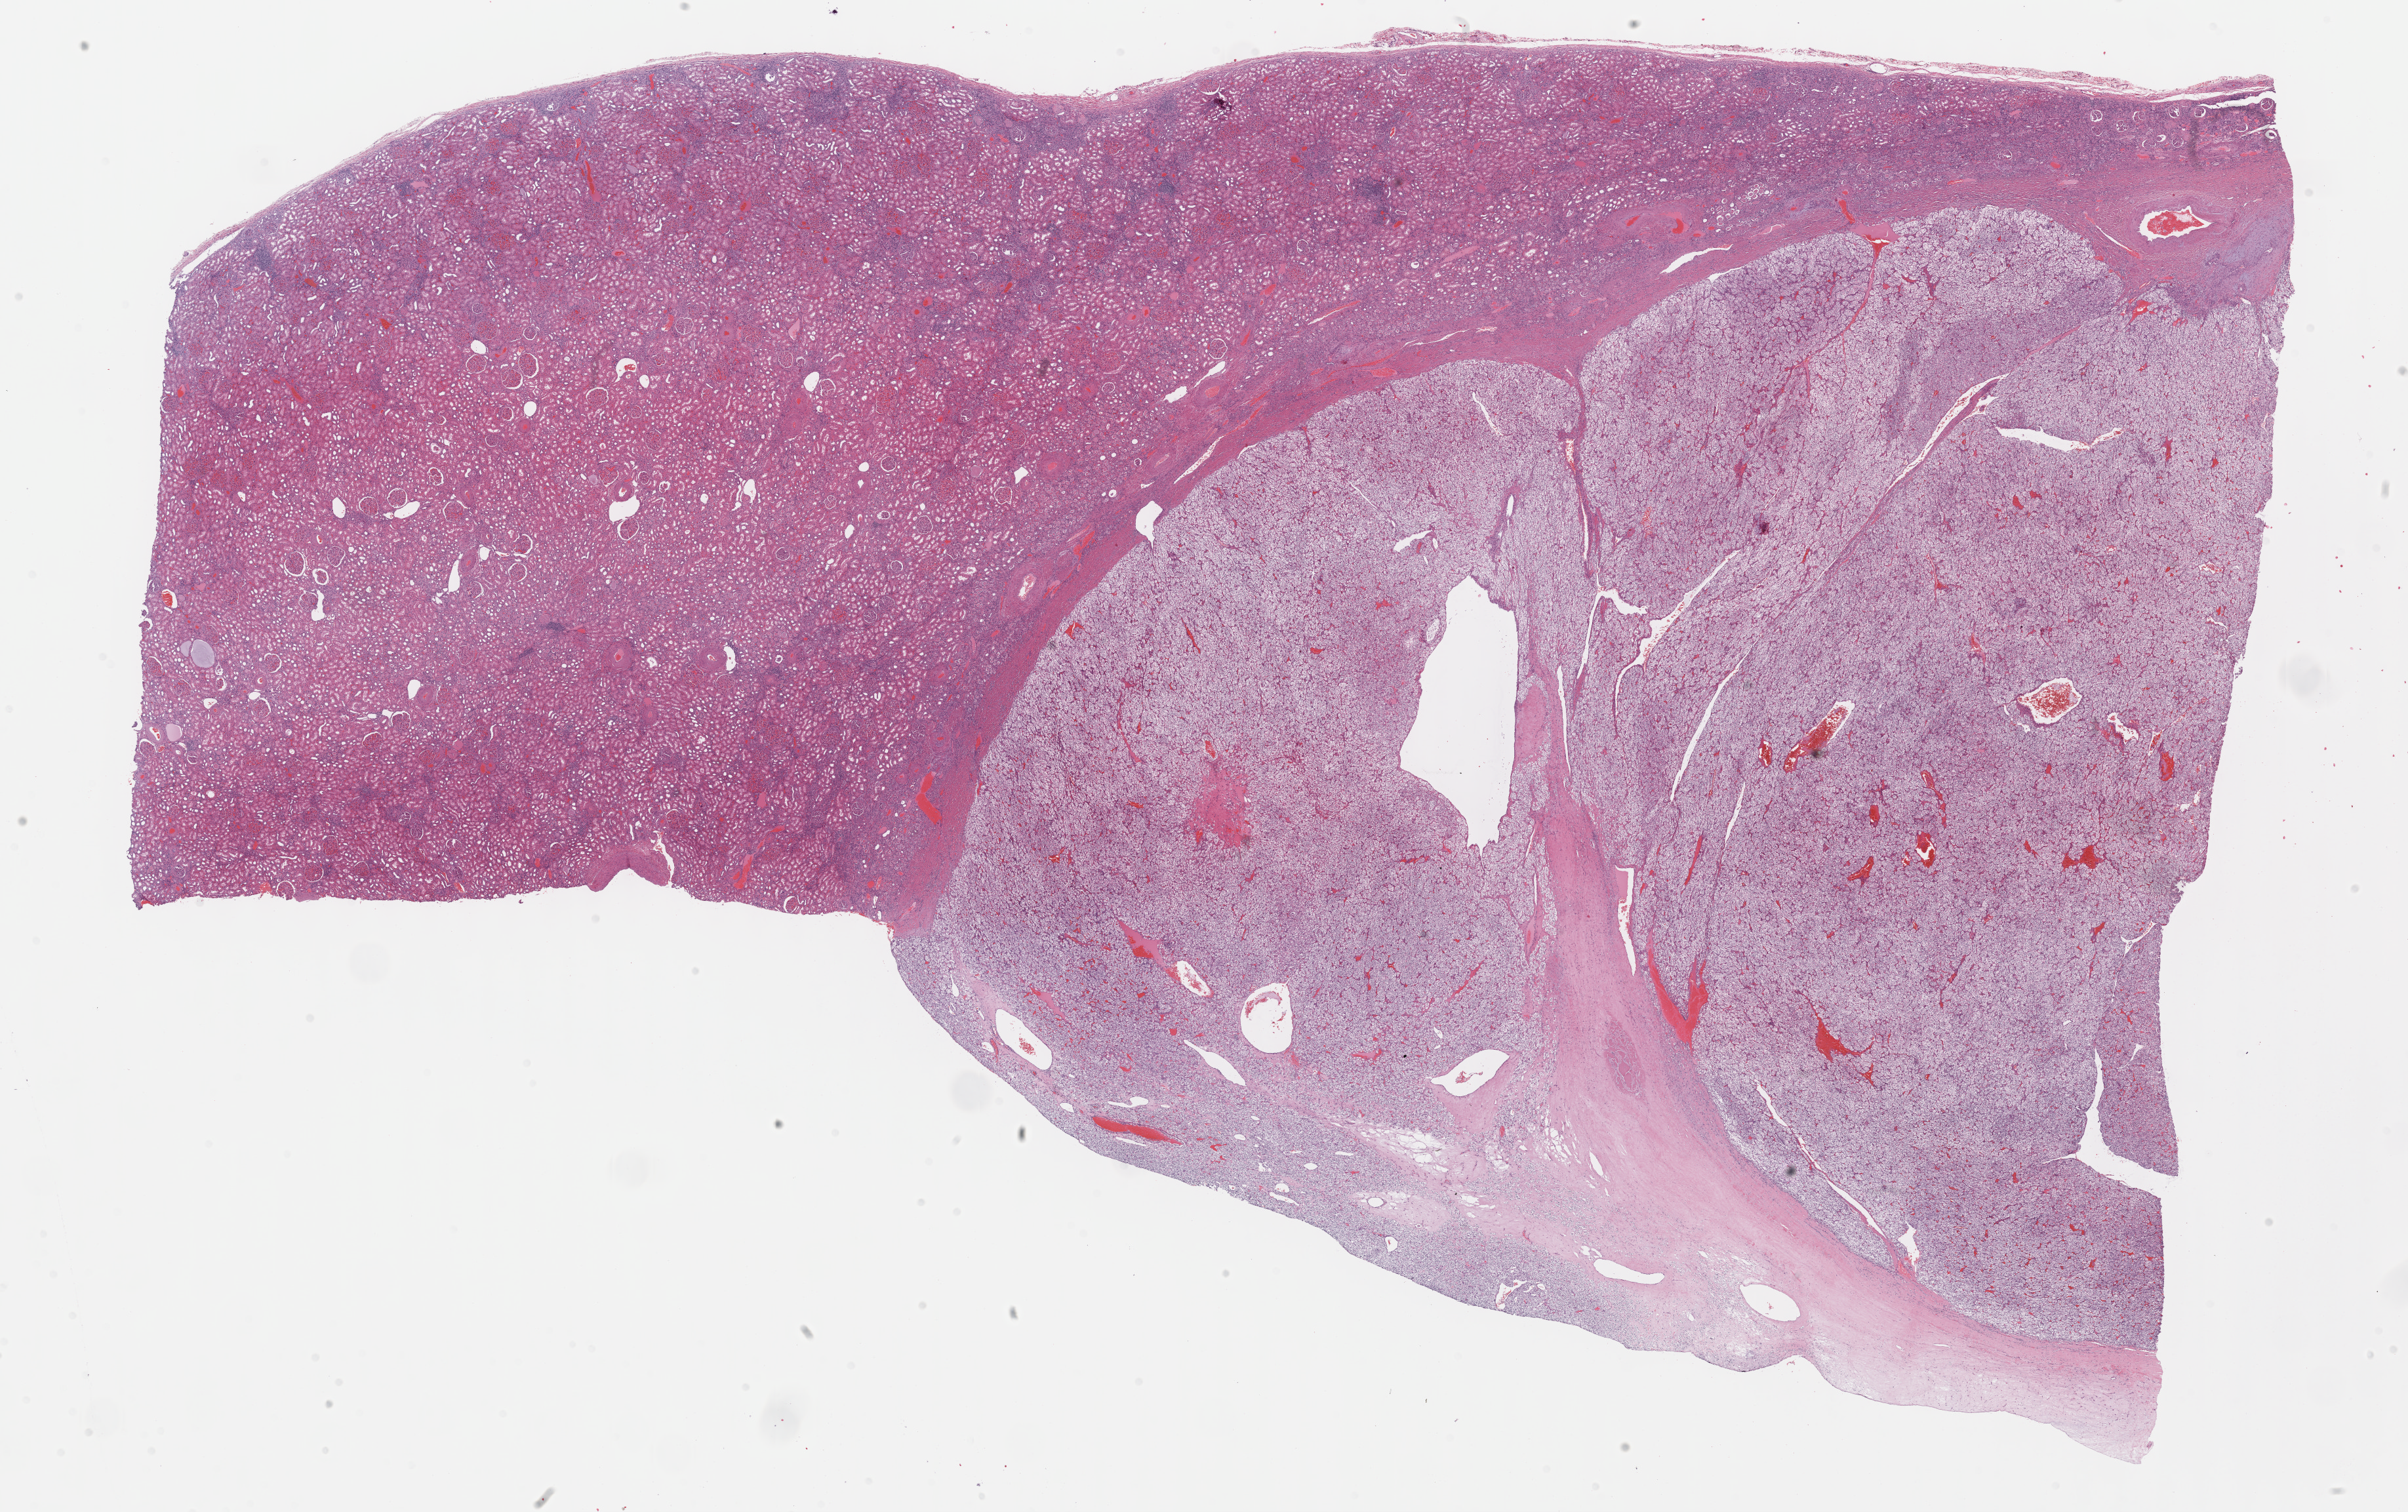
Whole-slide histology image, H&E, whole scanned area (about 29.7 x 18.7 mm, slide scanned at 40x) shown as a low-resolution overview. Formalin-fixed paraffin-embedded (FFPE) diagnostic section. Sample: primary tumour, kidney. Female patient; age at initial diagnosis 62 years. Histologic grade: G3 (poorly differentiated).
TNM: T1b NX MX. Diagnosis: Clear cell adenocarcinoma, NOS. AJCC pathologic stage: I.